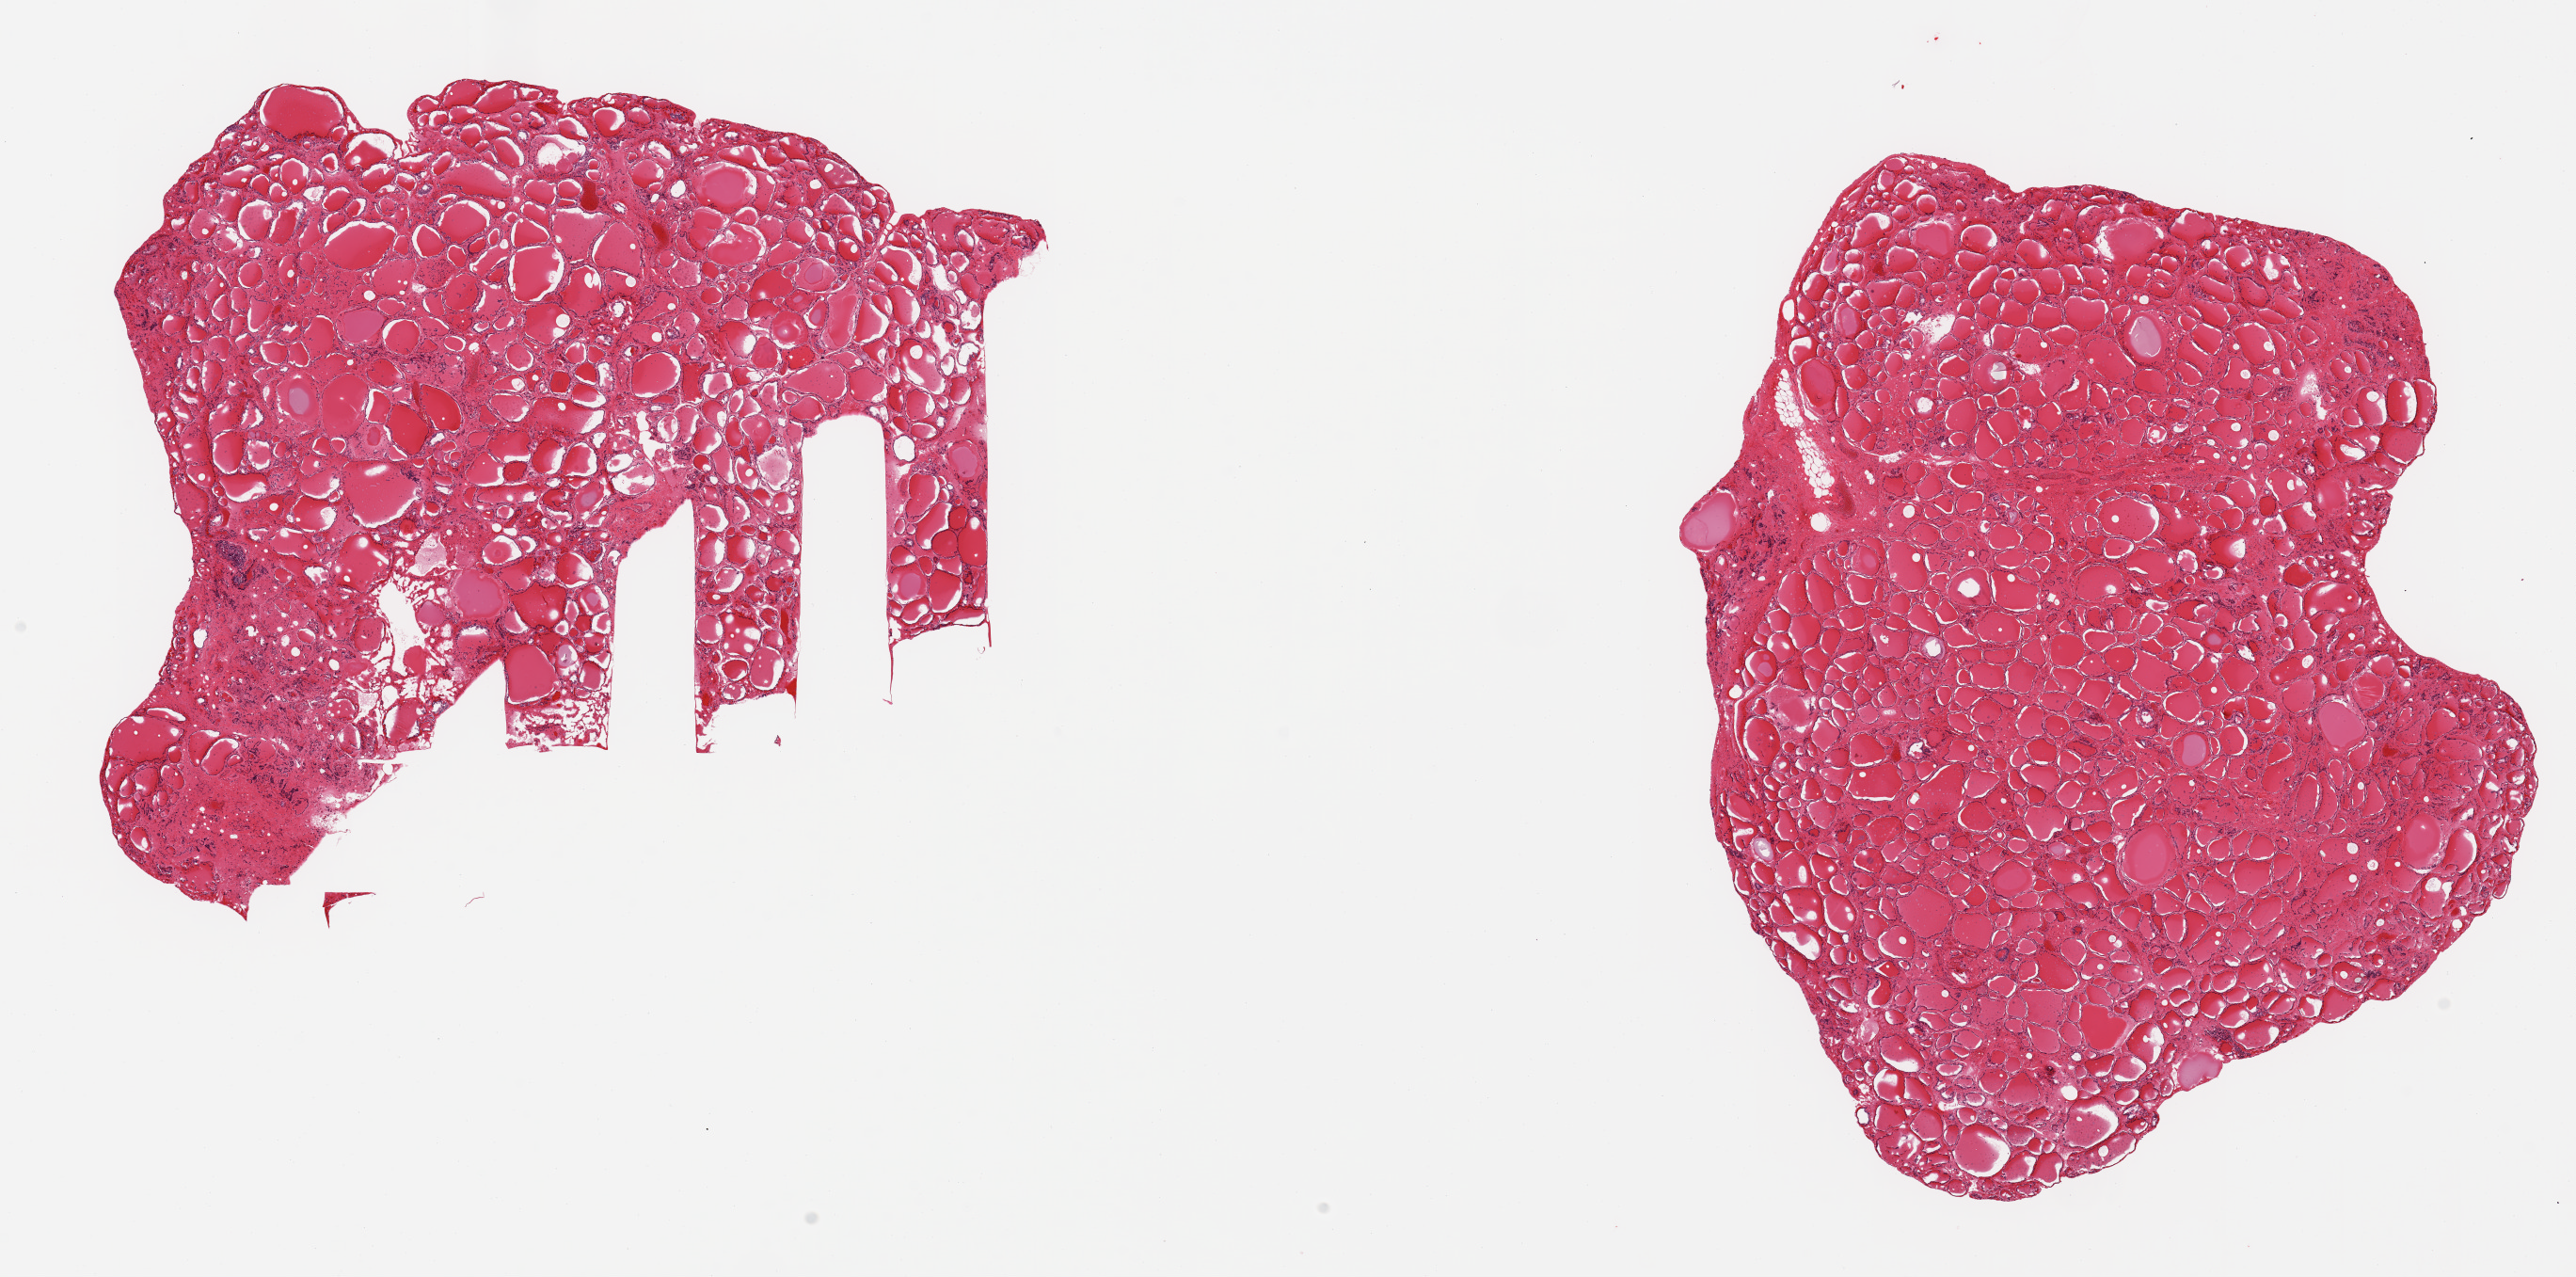
Whole-slide image, H&E stain, brightfield, whole scanned area (about 21.7 x 10.7 mm) shown as a low-resolution overview, PAXgene-fixed, paraffin-embedded tissue, section of thyroid (target tissue), tissue donor sample.
* reviewer comment on this tissue sample: 2 pieces; one with ~10% stromal fibrosis; focal granulomatous reaction with multinucleated giant cells; the second piece shows mild interstitial fibrosis